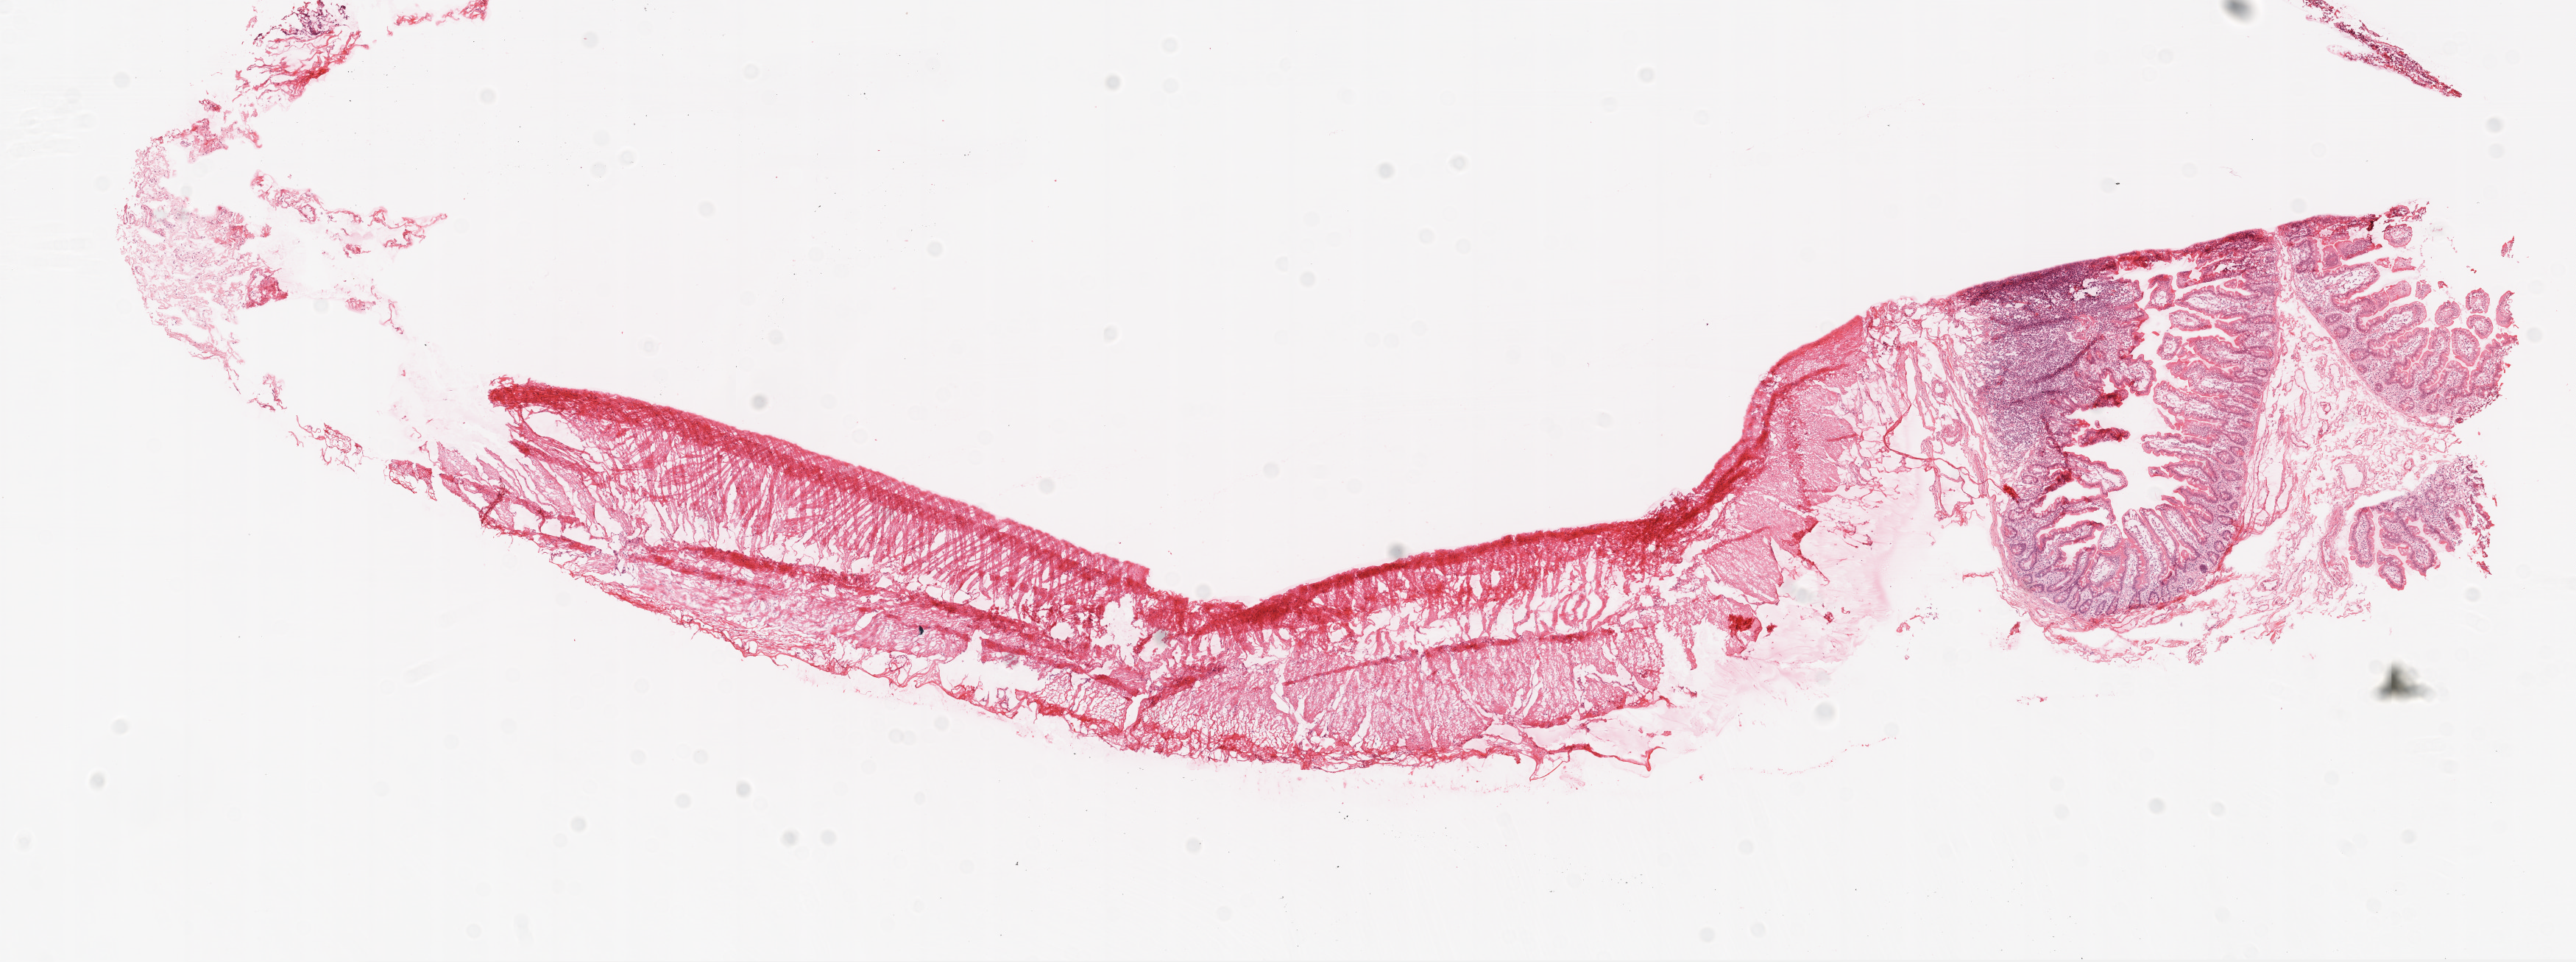
Whole-slide histology image, H&E-stained, whole scanned area (about 14.0 x 5.2 mm, acquisition: 20x scan) shown as a low-resolution overview; frozen section from the top of the tissue portion; solid tissue normal (non-tumour tissue) sample from the ovary. Female, age 61 years at initial diagnosis.
This section: solid tissue normal sample (biorepository sample class). Patient diagnosis: Serous cystadenocarcinoma, NOS.